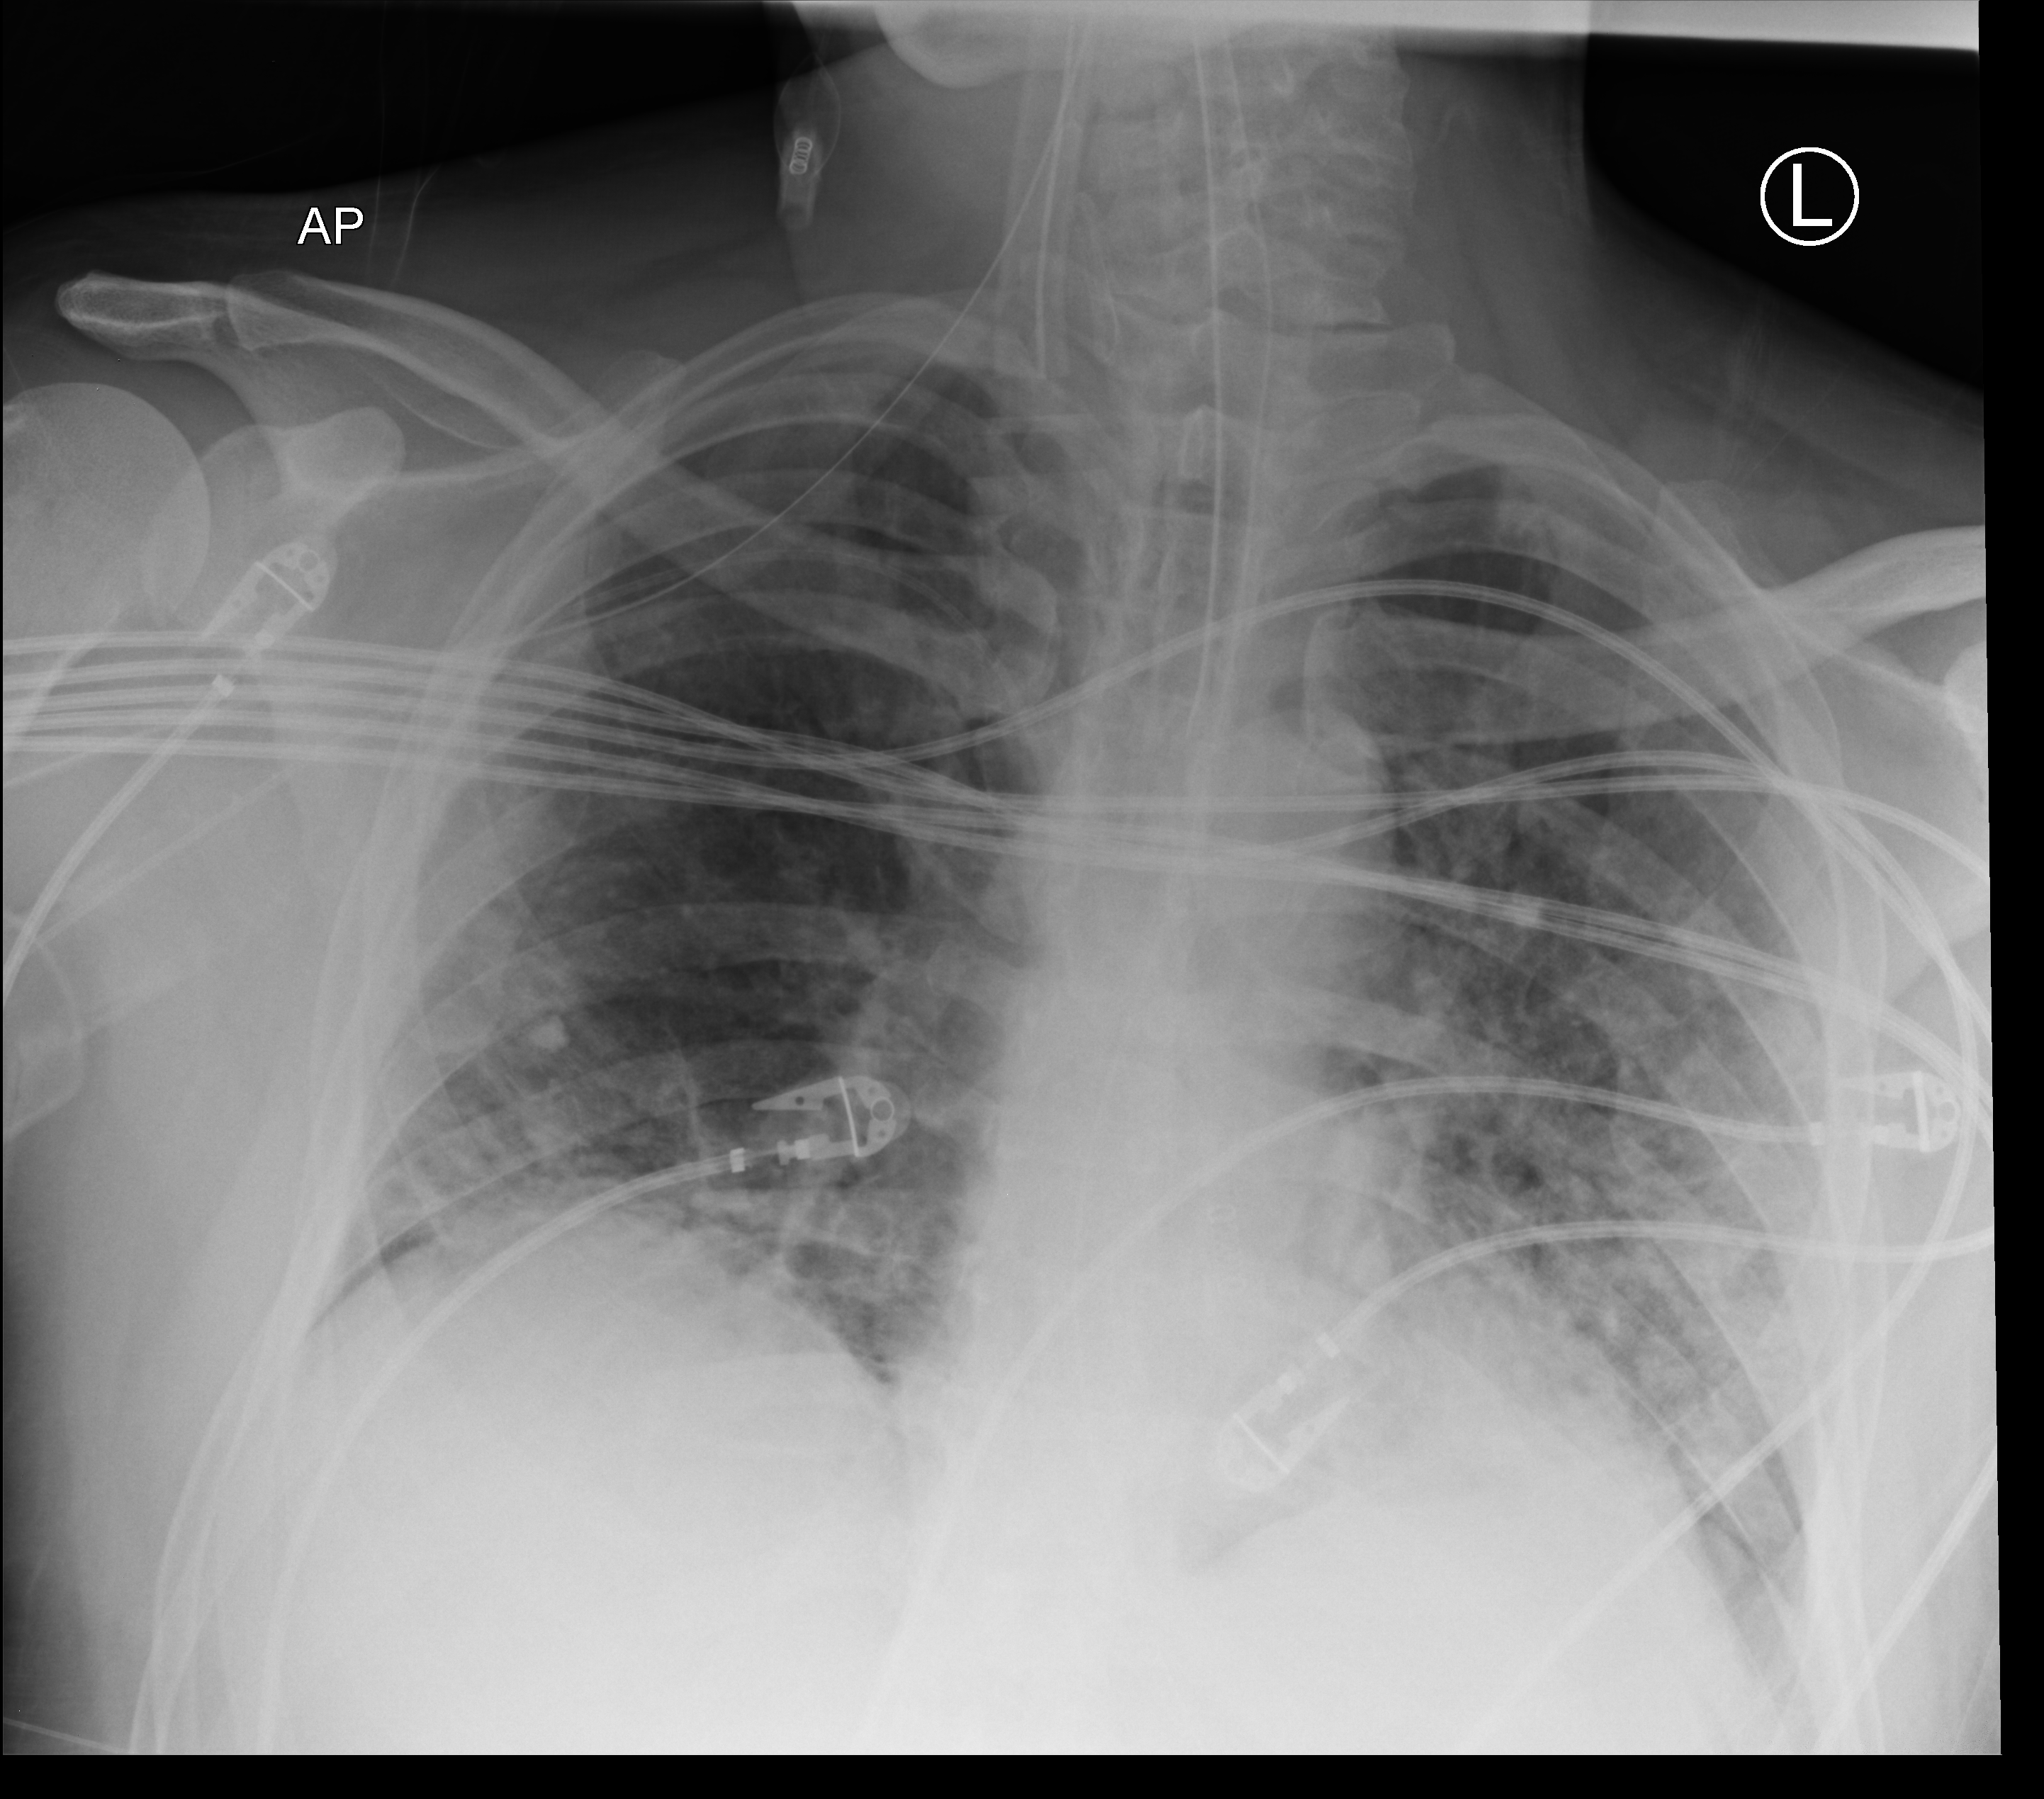
Bedside chest radiograph (computed radiography); anteroposterior (AP) projection. Male patient hospitalised with COVID-19, age 18–59 years.
From the hospital-stay record, not from the radiograph (when in the stay this image was taken is not recorded):
- hypertension (admission record): no